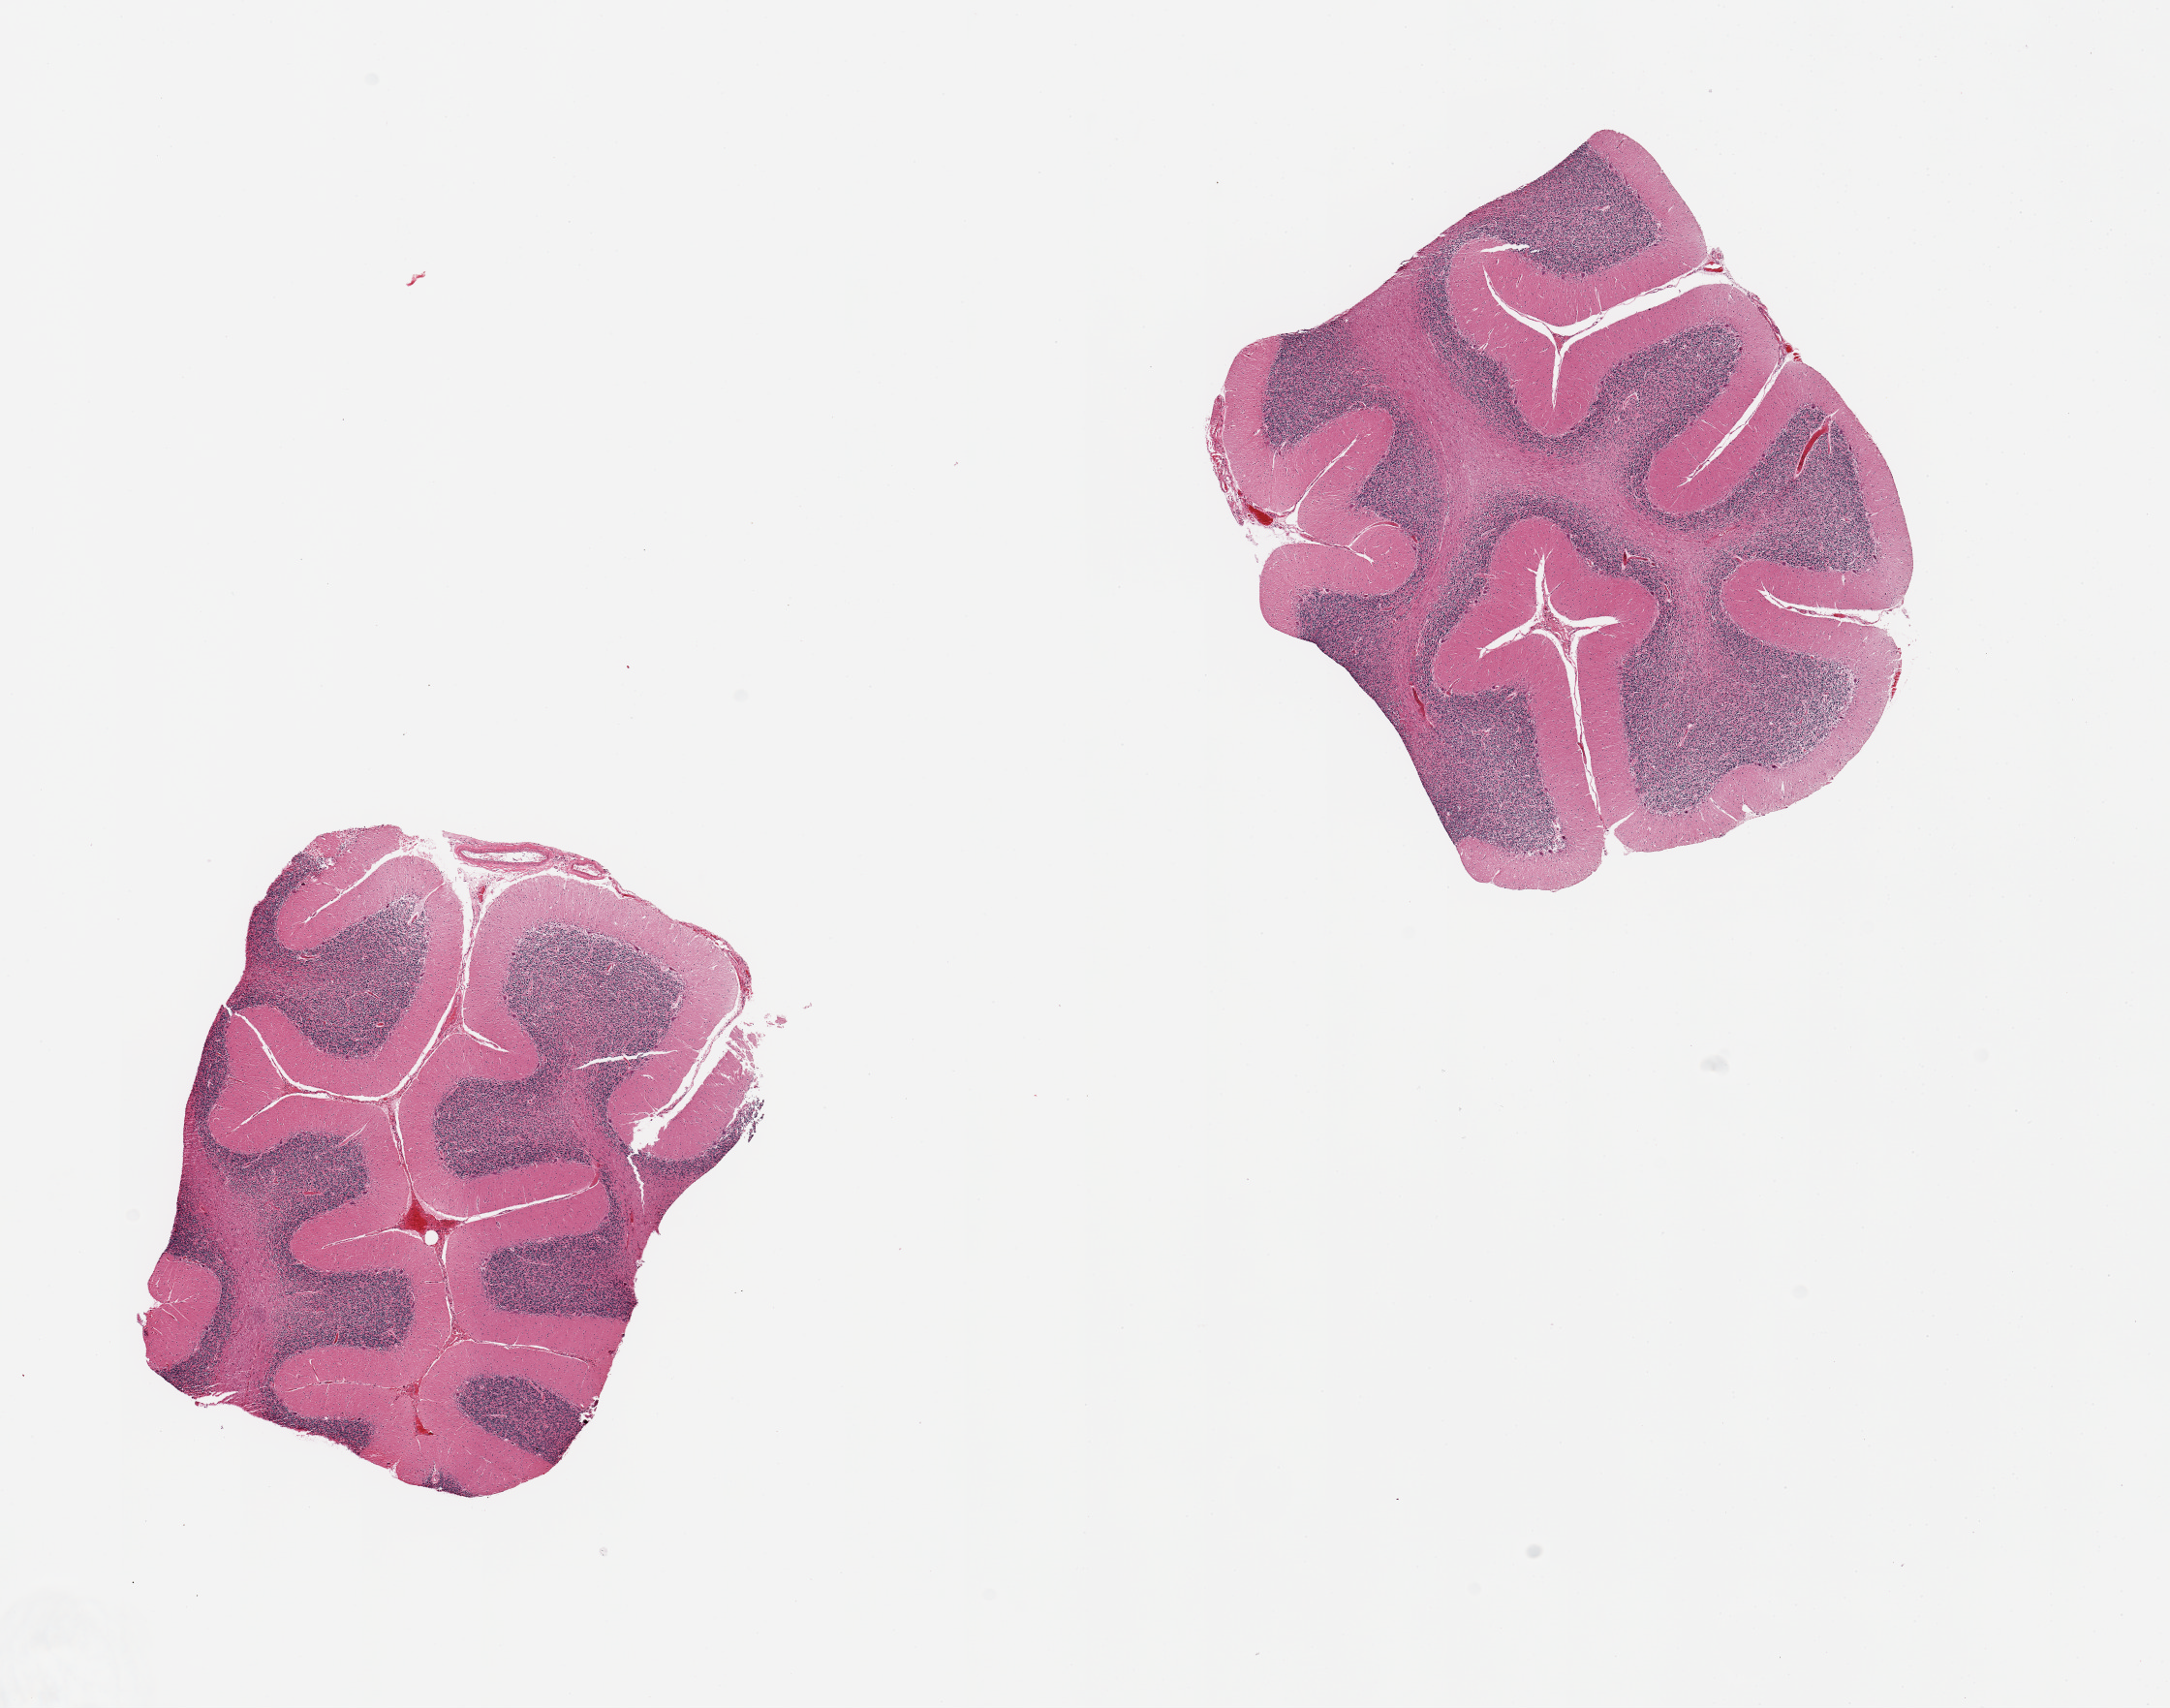
Digitized H&E-stained section, whole scanned area (about 17.7 x 13.9 mm, slide scanned at 20x) shown as a low-resolution overview. PAXgene-fixed, paraffin-embedded tissue. Target tissue: cerebellum. Donor tissue sample.
* reviewer comment on this tissue sample: 2 pieces; target is 4